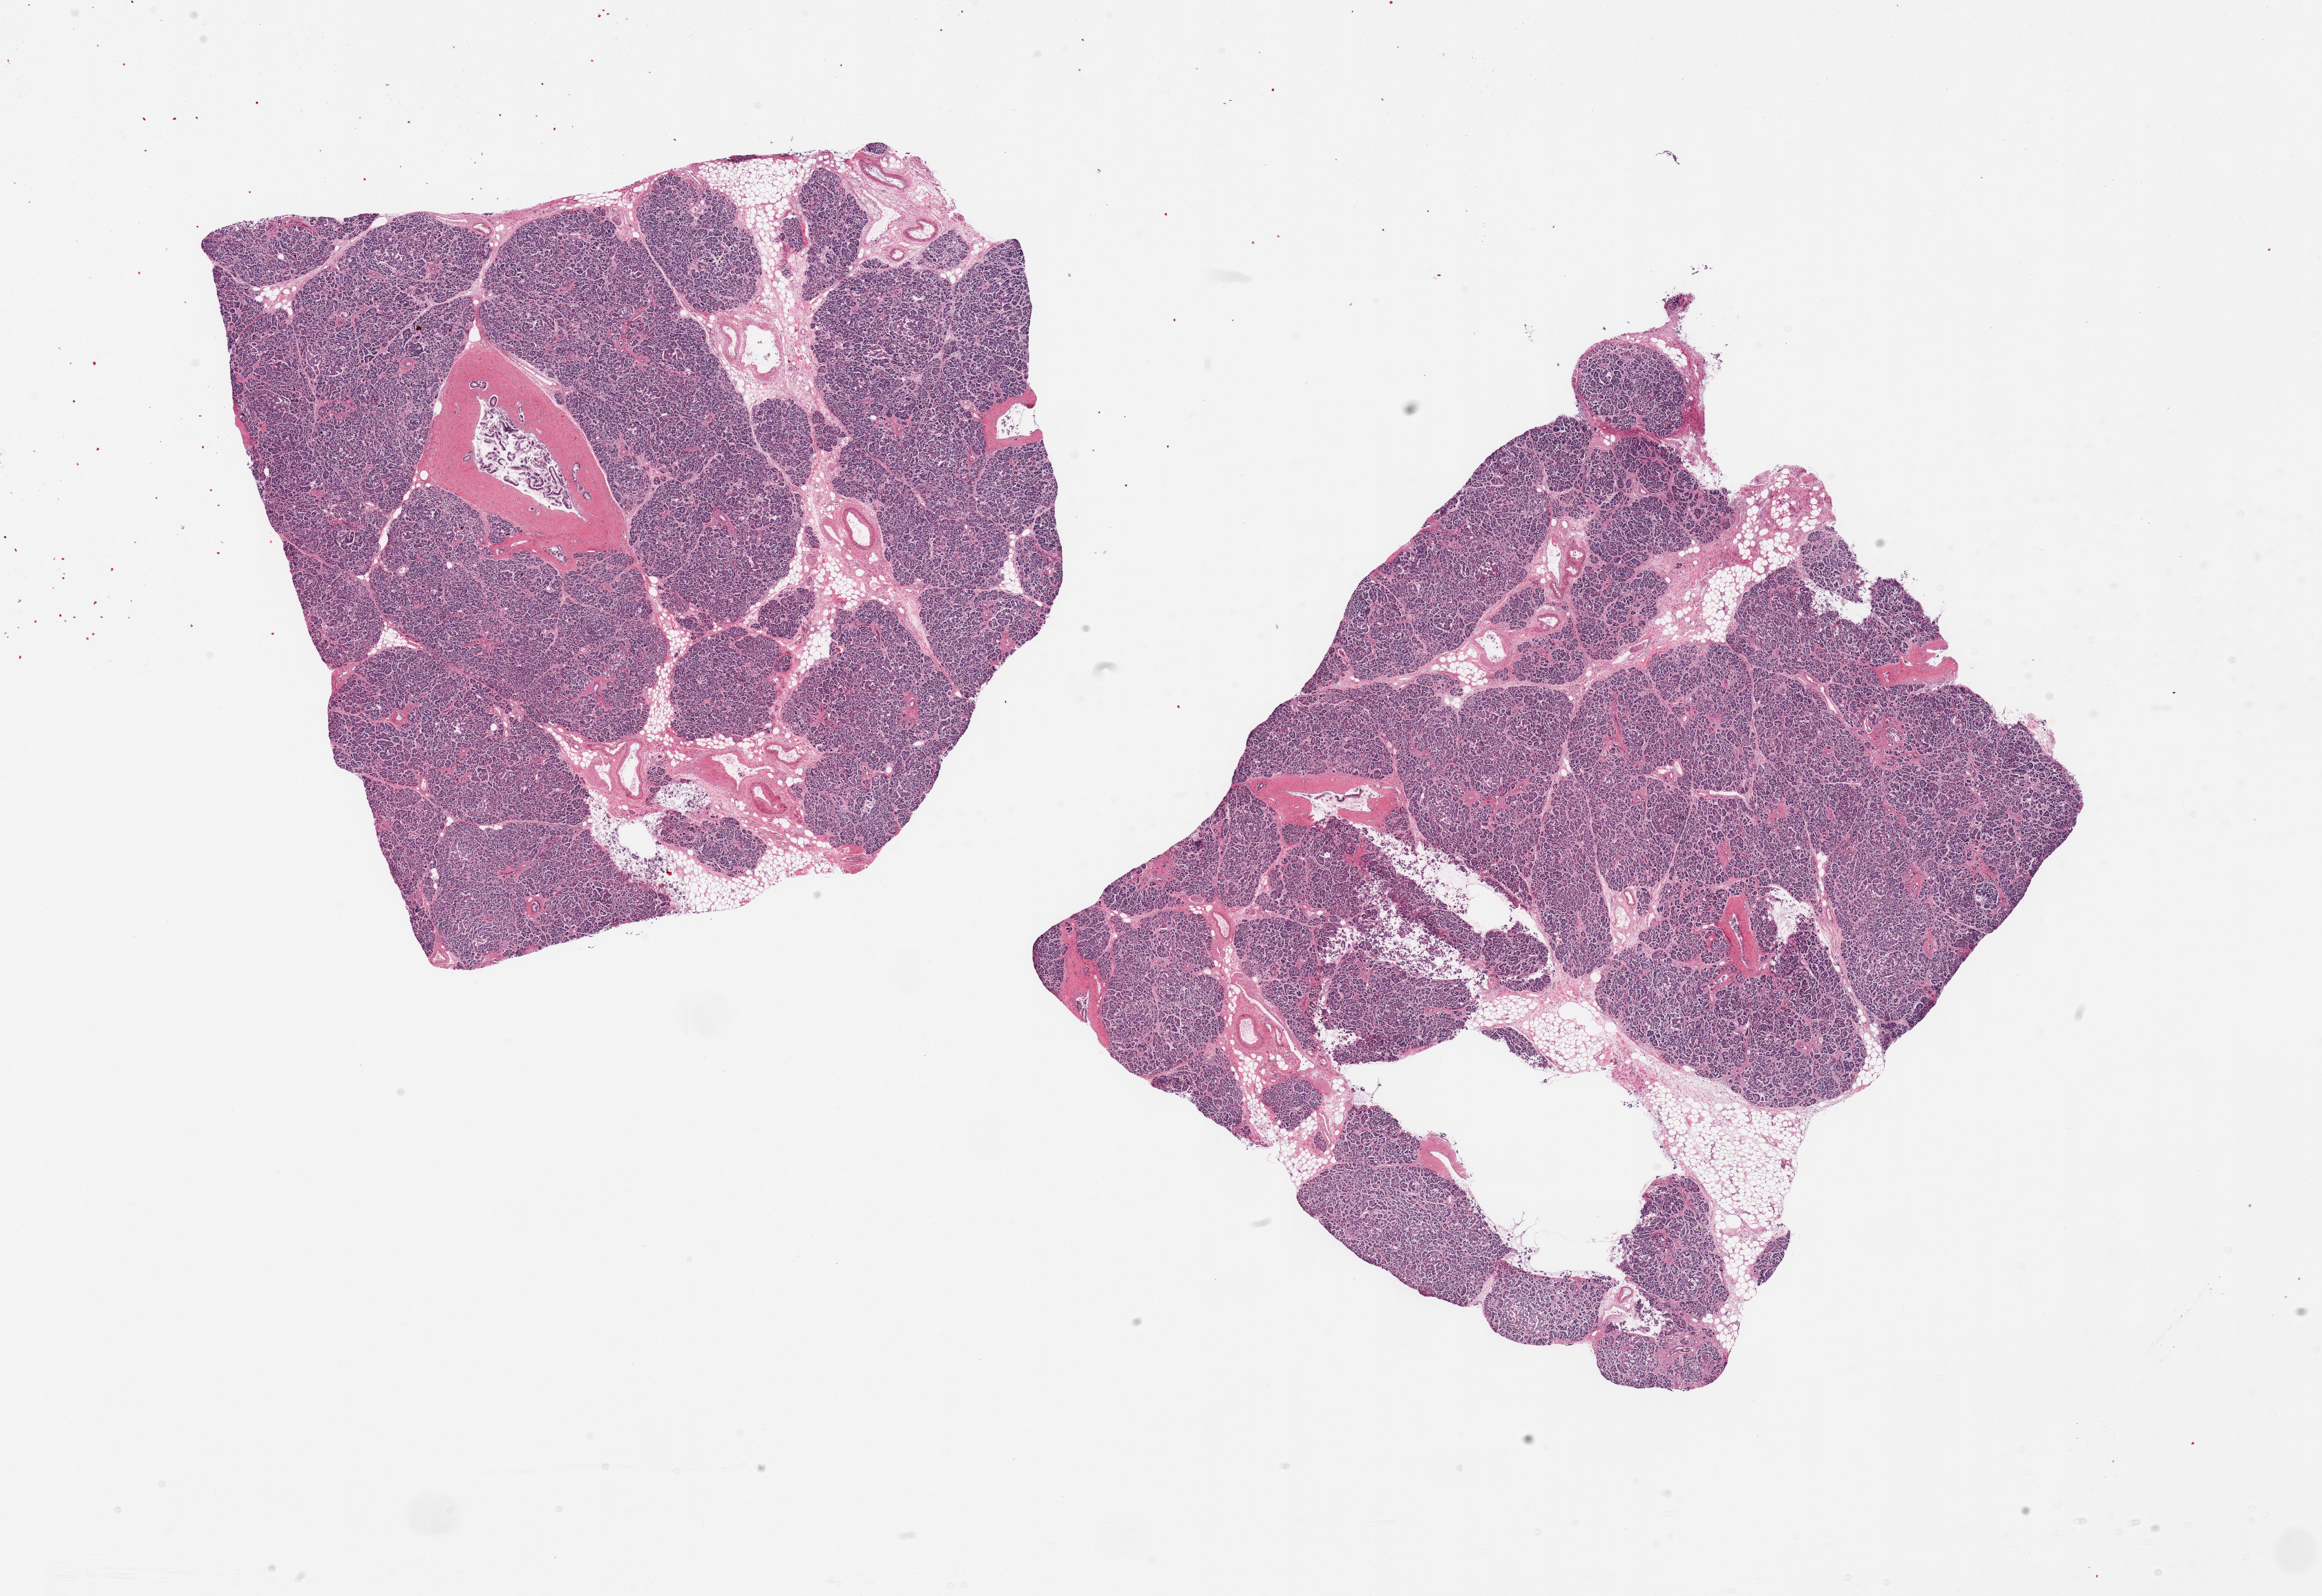
Hematoxylin and eosin (H&E) whole-slide image, whole scanned area (about 26.6 x 18.3 mm) shown as a low-resolution overview, PAXgene-fixed, paraffin-embedded tissue, sampled site (target tissue): pancreas, donor tissue sample. Male donor.
Review note (as recorded): 2 pieces, moderately advanced autolysis.